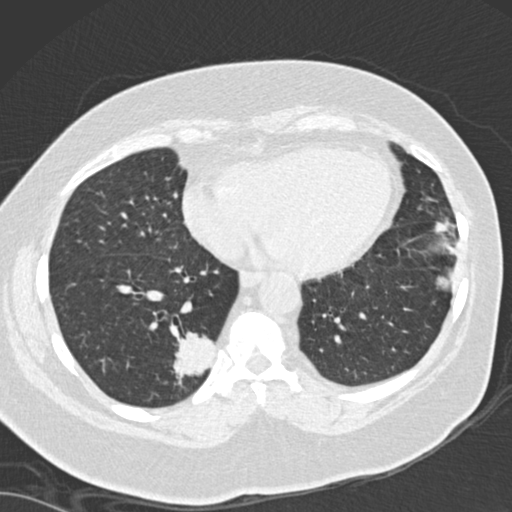
Low-dose screening chest CT, one axial slice; position 56 of 162 along the scan axis; 120 kVp; lung window (W 1500 / L -600 HU); 512 × 512 image matrix, field of view 328 × 328 mm.
Structures marked on this image (expert manual segmentation):
- lesion 1 (tumor, lower lobe of right lung): bounding box <173,331,216,385> (left, top, right, bottom; pixels)